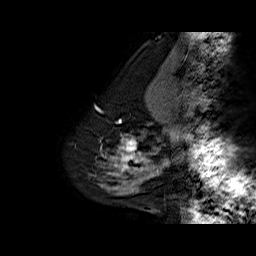
Breast MRI (dynamic contrast-enhanced), one sagittal slice. Slice 14 of 60 in the series (ordered by position). Dynamic contrast-enhanced series, time point 2 of 6 at this slice position (early post-contrast). 1.5 T. TE 6.3 ms, TR 32.5 ms. 256 × 256 image matrix, field of view 200 × 200 mm. Female patient. From the clinical record (not read from this slice): setting: breast cancer imaged before/during neoadjuvant chemotherapy; receptor status: triple-negative.
Outlined on this slice (semi-automatic segmentation, software-assisted and operator-edited):
- analysis volume of interest (the breast-tissue region the enhancement analysis was run in; not a lesion): bounding box [x1, y1, x2, y2] px = [108, 134, 154, 177]
- tumour enhancement mask (voxels above the 100 % enhancement threshold inside the analysis volume of interest): [118, 139, 153, 176]